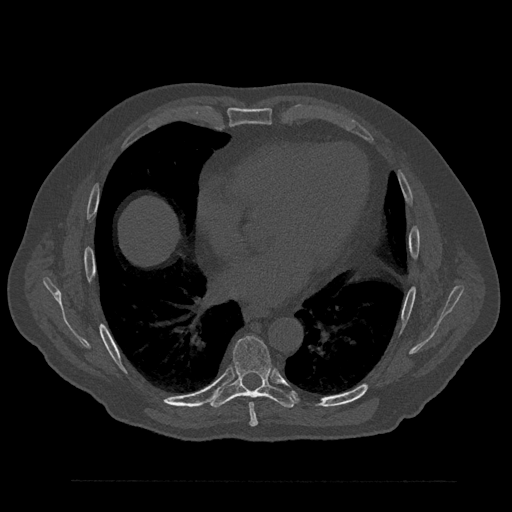
CT including the spine, one axial slice; slice 468 of 797 in the series (ordered by position); reconstruction kernel Br40s/3; bone window (W 1800 / L 400 HU); 0.5 mm slice thickness; 512 × 512 image matrix, field of view 430 × 430 mm. Male patient, age 61 years. Case-level facts recorded for this patient, not image findings: primary cancer: prostate.
Structures marked on this image (semi-automatically segmented with operator editing):
- T7 vertebra: box from (x=249, y=402) to (x=258, y=427) px
- T8 vertebra: (x=210, y=336)–(x=296, y=408)